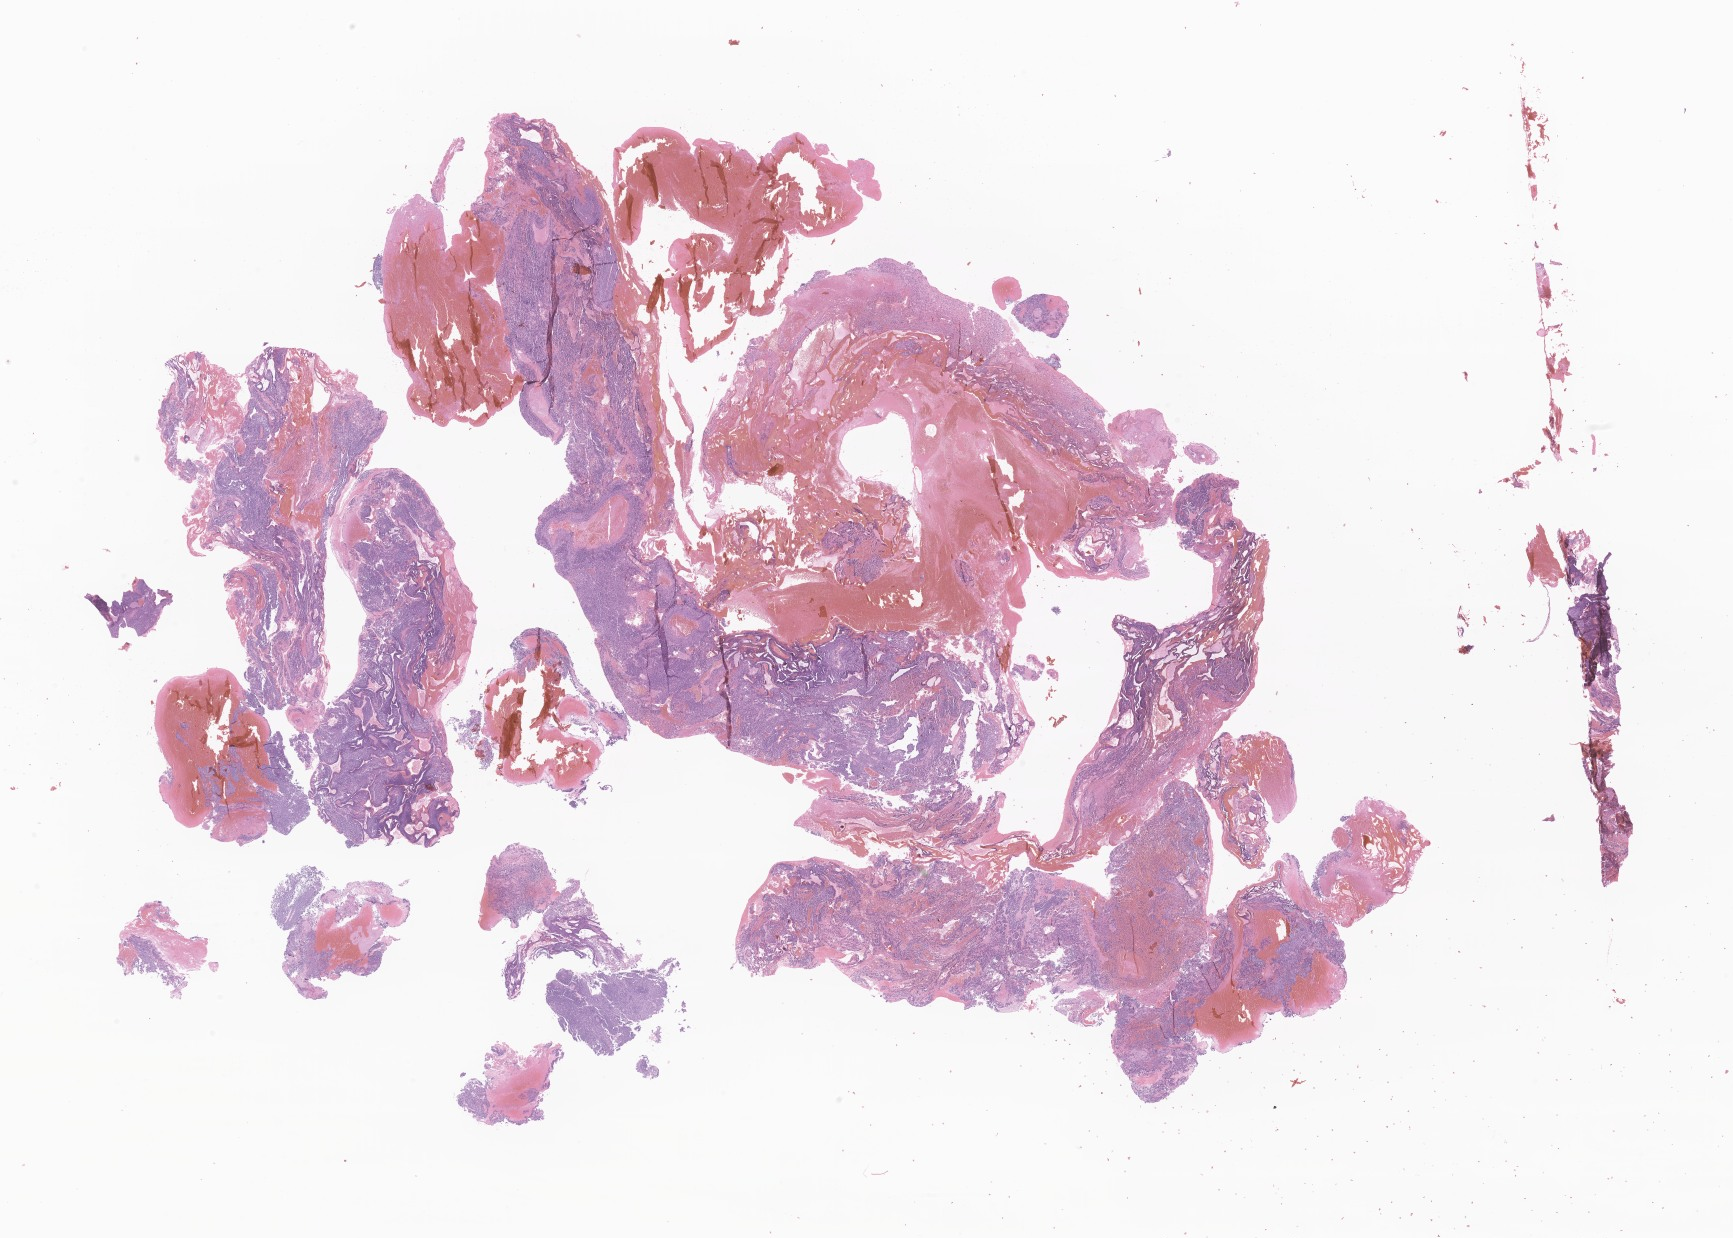
Hematoxylin and eosin (H&E) whole-slide image of tumor tissue from the brain — low-resolution overview of the scanned area, about 29.2 x 20.9 mm; formalin-fixed paraffin-embedded section. Patient female; age 193 months (16 years 1 month).
Diagnosis: Medulloblastoma, NOS.